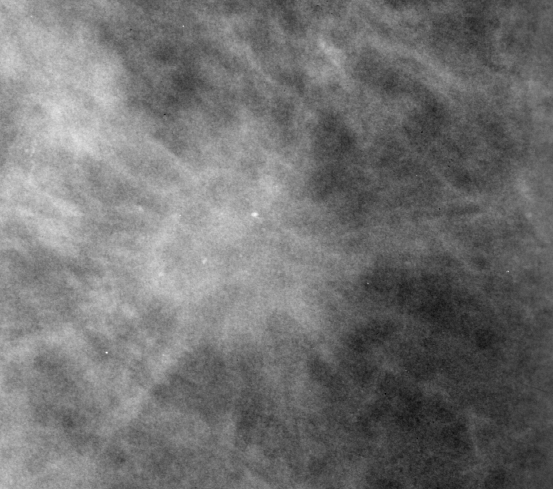
Region of interest cut from a scanned film mammogram (one marked finding); right breast; CC view; BI-RADS breast density category 3 (scale 1–4).
- Finding: calcifications, morphology punctate, distribution clustered; BI-RADS assessment category 4; pathology result (as recorded, not read from the image): malignant.